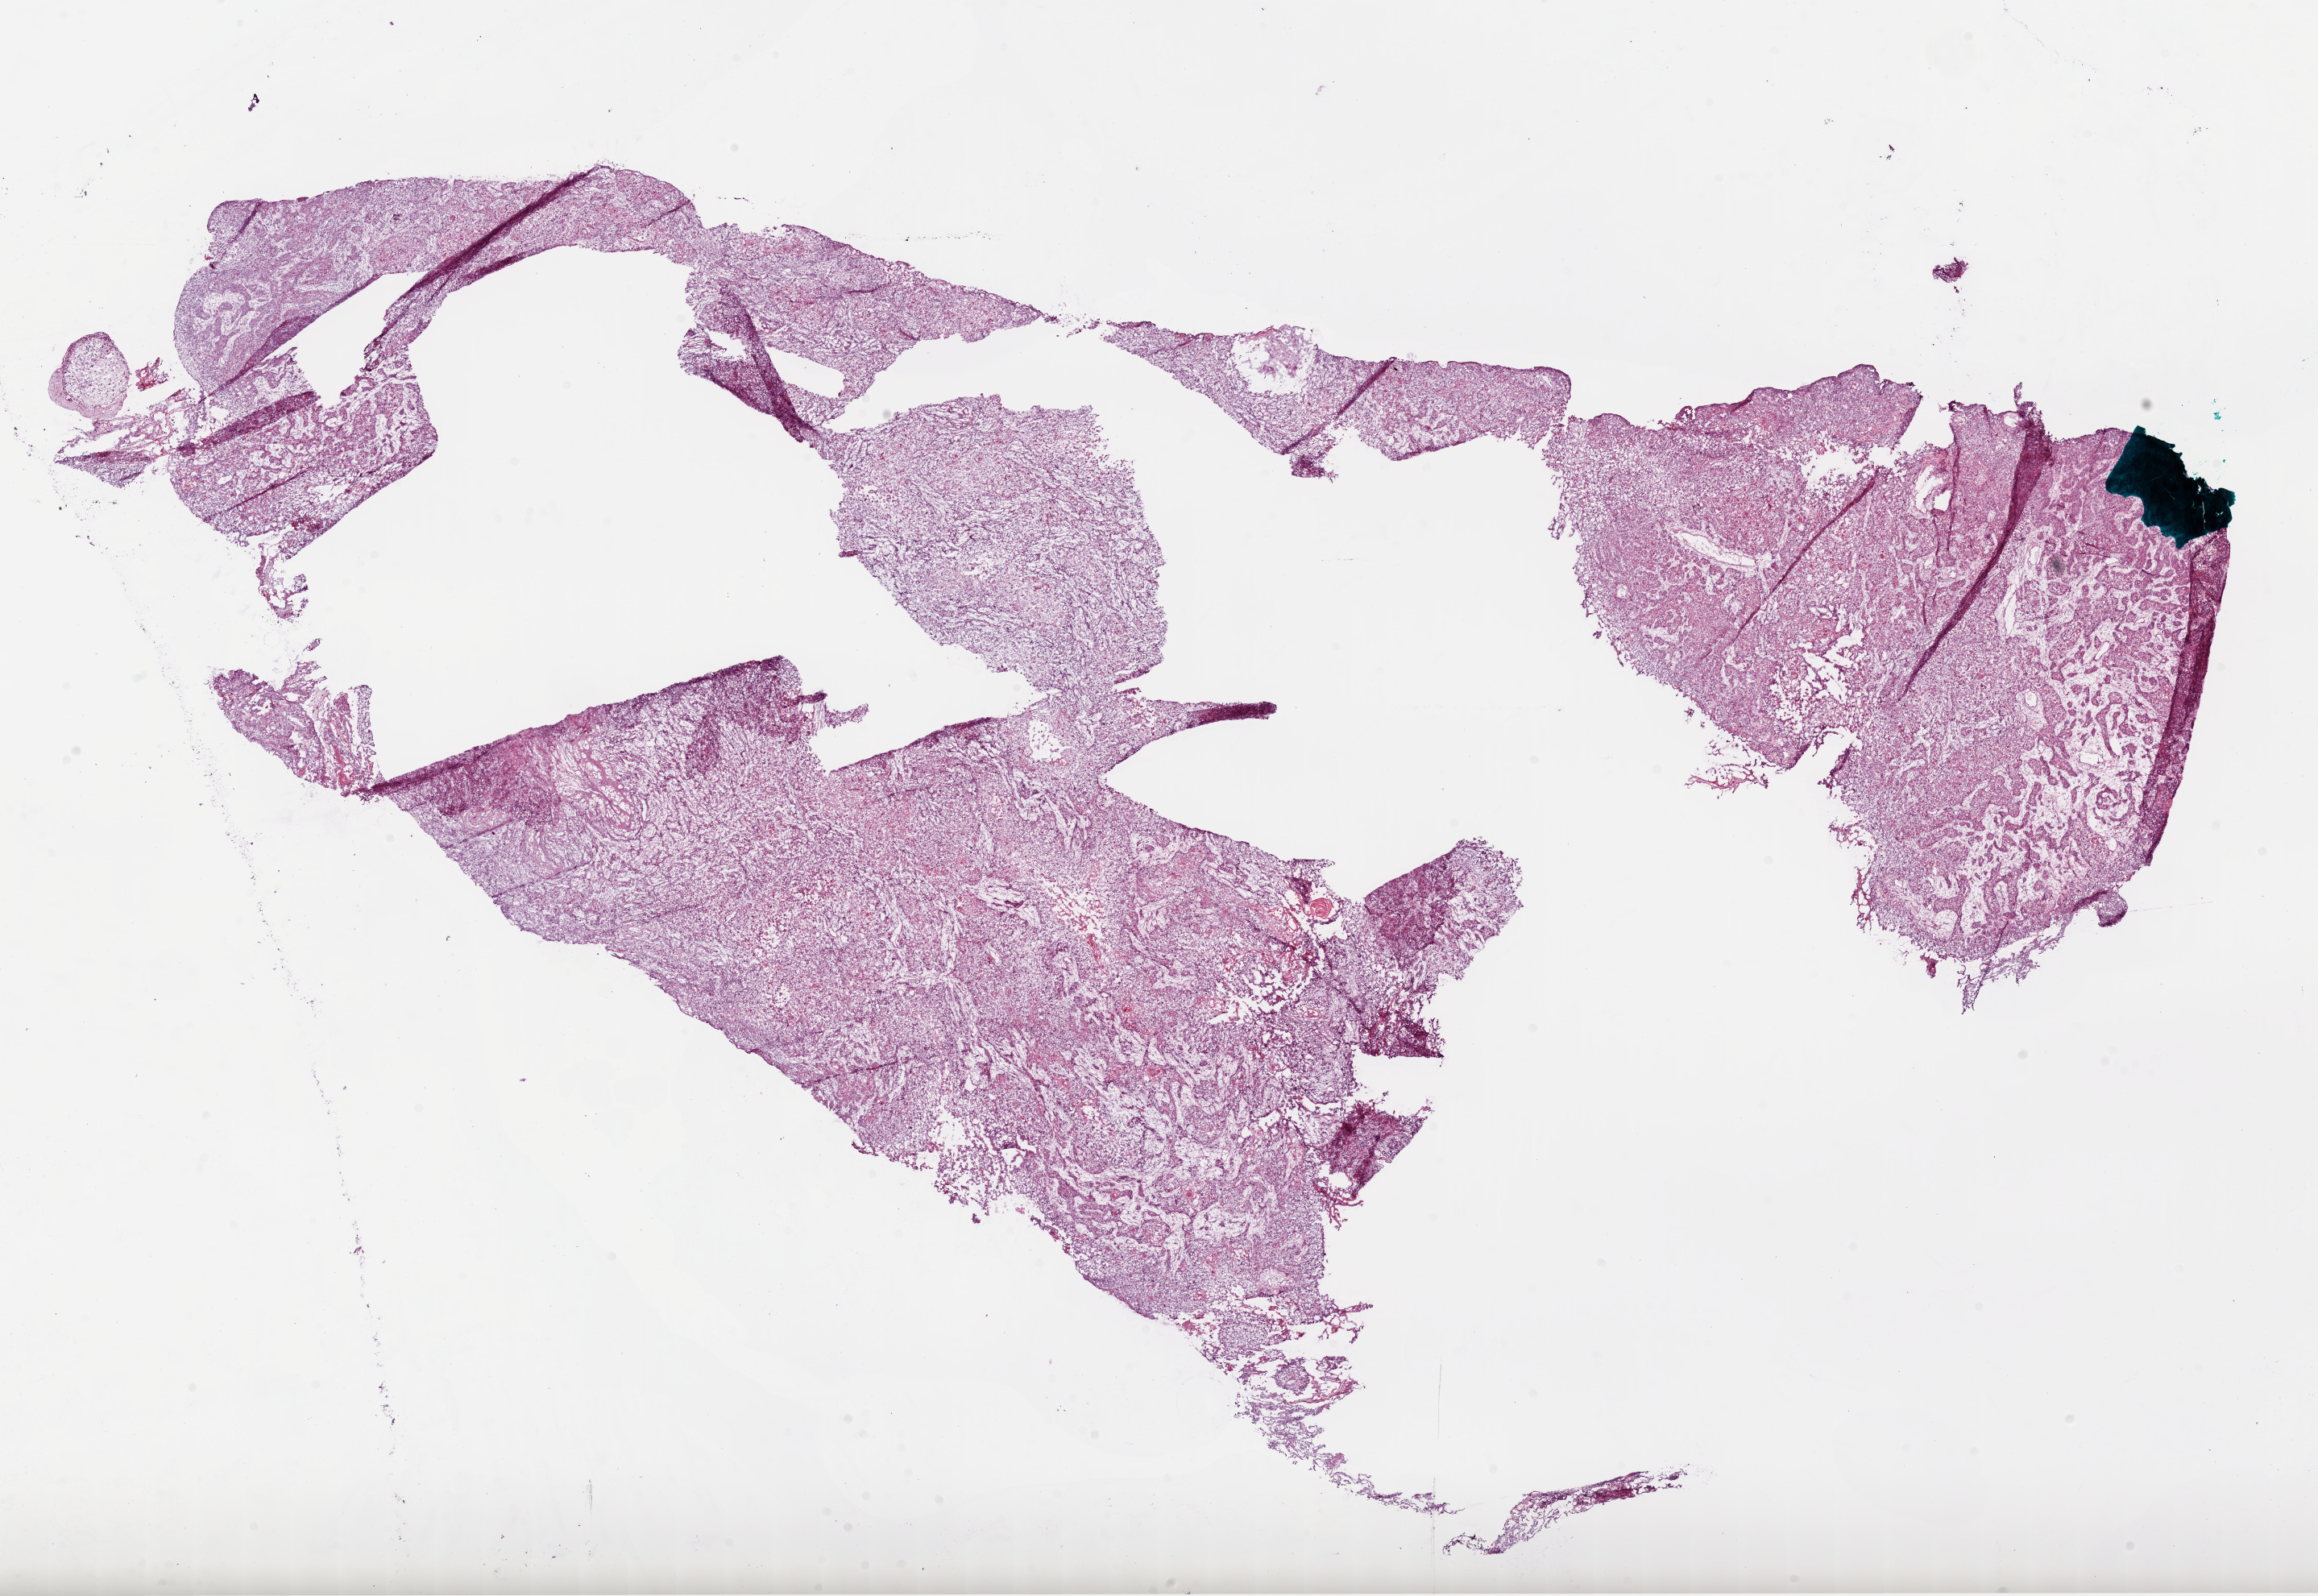
H&E-stained whole-slide image — low-resolution overview of the scanned area, about 23.2 x 16.0 mm; frozen section from the bottom of the tissue portion; sample: primary tumour, lung. Male, age 71 years at initial diagnosis. Slide review estimates, as recorded: tumour nuclei 70%, necrosis 0%.
- histologic diagnosis: Squamous cell carcinoma, NOS (upper lobe, lung)
- AJCC pathologic stage: IIIA